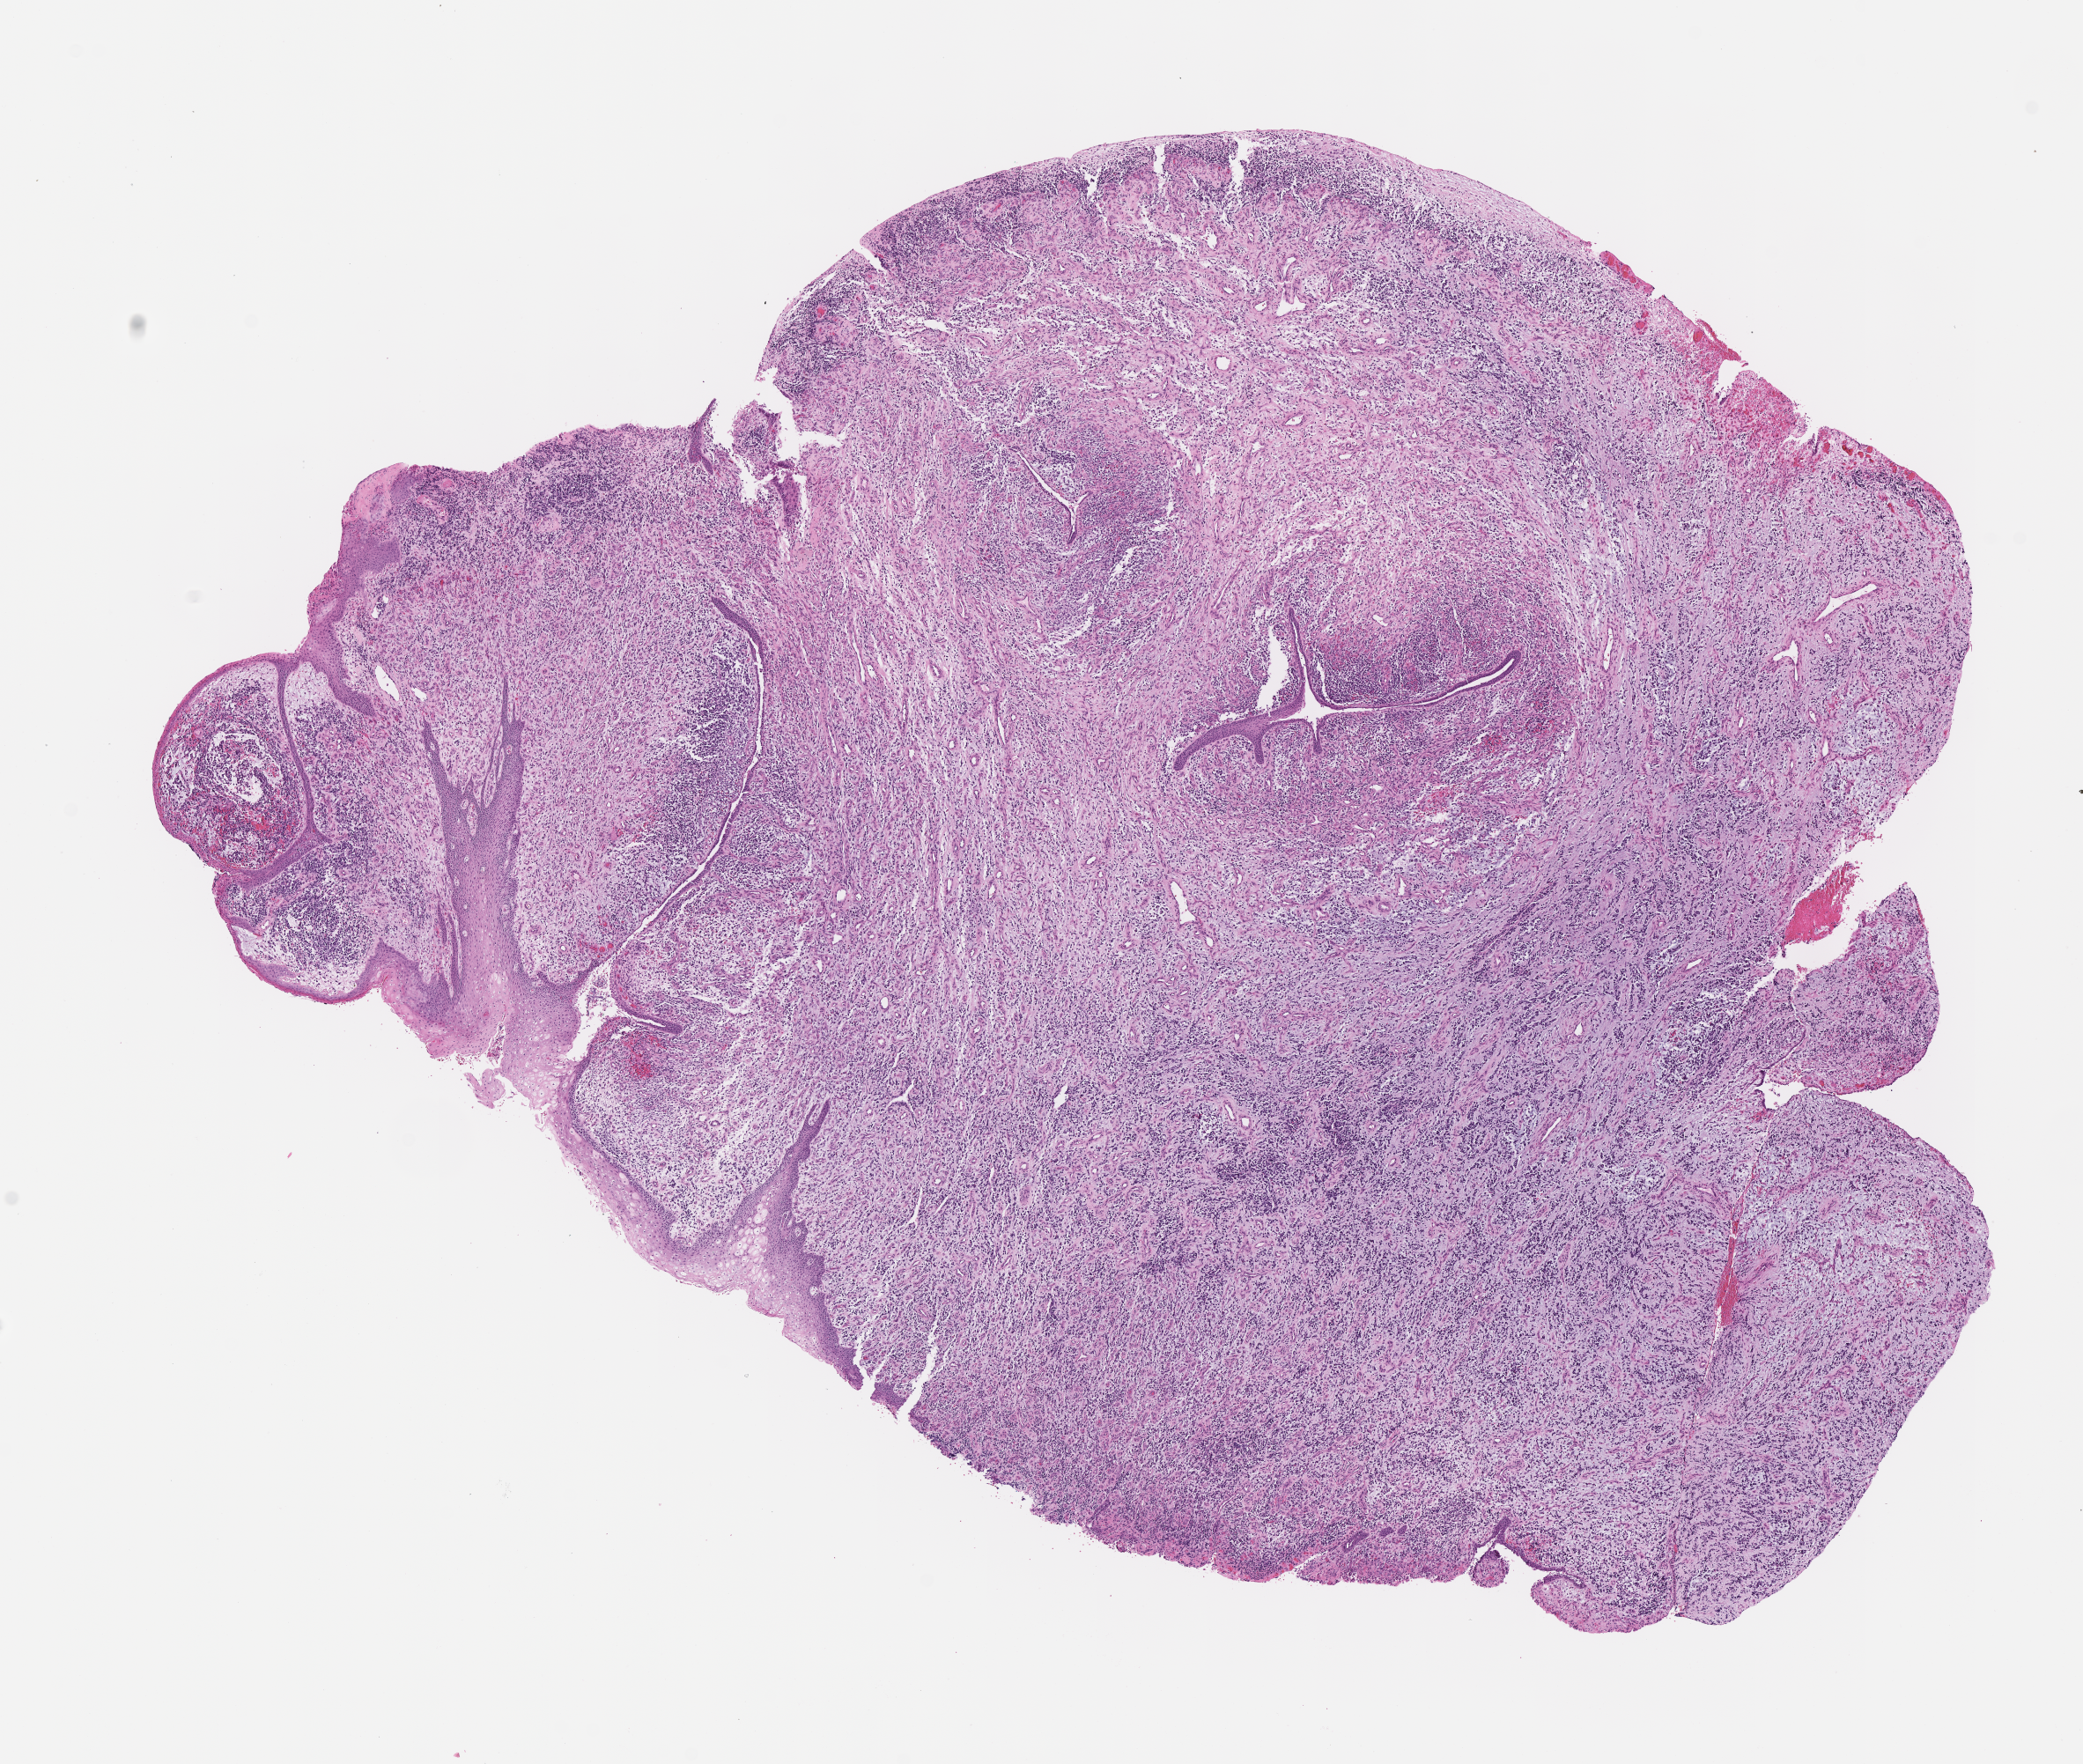
Digitized hematoxylin and eosin (H&E)-stained section of tumor tissue, shown as a low-resolution overview of the whole scanned area (about 9.6 x 8.1 mm); FFPE section; site: vagina. Female patient, age at diagnosis 4.1 years.
• metastatic status at presentation (as recorded): non-metastatic (confirmed)
• stage (as recorded): 1
• diagnosis: rhabdomyosarcoma; histological classification: embryonal rhabdomyosarcoma